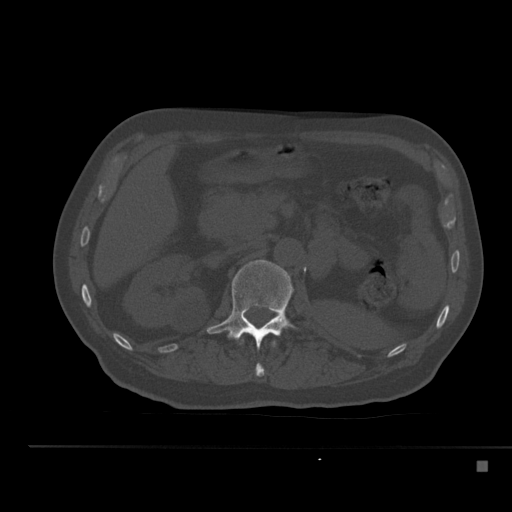
CT including the spine, one axial slice. Position 208 of 517 along the scan axis. Reconstruction kernel Br40s. 120 kVp. Bone window (W 1800 / L 400 HU). 1.5 mm slice thickness. 512 × 512 image matrix, field of view 408 × 408 mm. Male patient, age 70 years. Case-level facts recorded for this patient, not image findings: primary cancer: renal; vertebrae with lytic lesions (as recorded): T4, T6, T10, T12, L3, L4, L5.
Structures marked on this image (semi-automatic segmentation, software-assisted and operator-edited):
- L1 vertebra: bounding box <206,260,297,349> (left, top, right, bottom; pixels)
- T12 vertebra: <239,337,276,377>